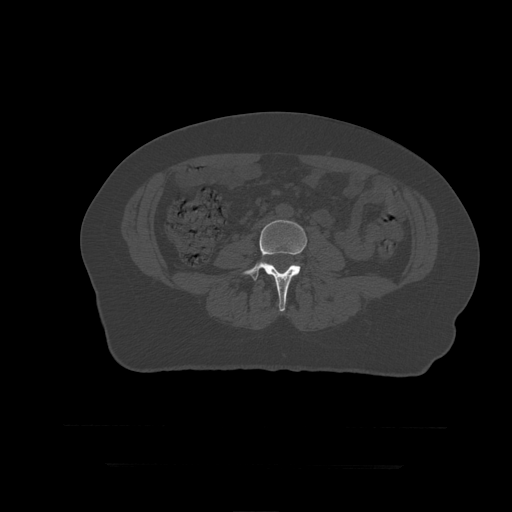
CT including the spine, one axial slice. Slice 95 of 399 in the series (ordered by position). Reconstruction kernel STANDARD. Bone window (W 1800 / L 400 HU). 512 × 512 image matrix, field of view 450 × 450 mm. Patient age 41 years. Case-level facts recorded for this patient, not image findings: primary cancer: breast.
Outlined on this slice (semi-automatic segmentation, software-assisted and operator-edited):
- L4 vertebra: box from (x=243, y=220) to (x=308, y=312) px